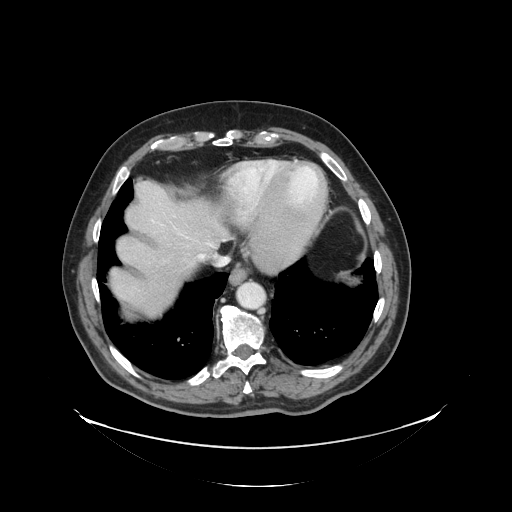
Contrast-enhanced abdominal CT, one axial slice. Position 118 of 138 along the scan axis. Reconstruction kernel STANDARD. 120 kVp. Intravenous contrast given. Soft-tissue window (W 400 / L 40 HU). 512 × 512 image matrix. Male patient, age 77 years. From the clinical record (not read from this slice): diagnosis: colorectal cancer liver metastases, imaged before liver resection; multiple liver metastases: no.
Outlined on this slice (outlined manually by an expert reader):
- hepatic veins: bounding box [x1, y1, x2, y2] px = [207, 243, 213, 246]
- liver: [110, 182, 226, 317]
- planned liver remnant (the part of the liver to remain after resection): [110, 183, 225, 290]